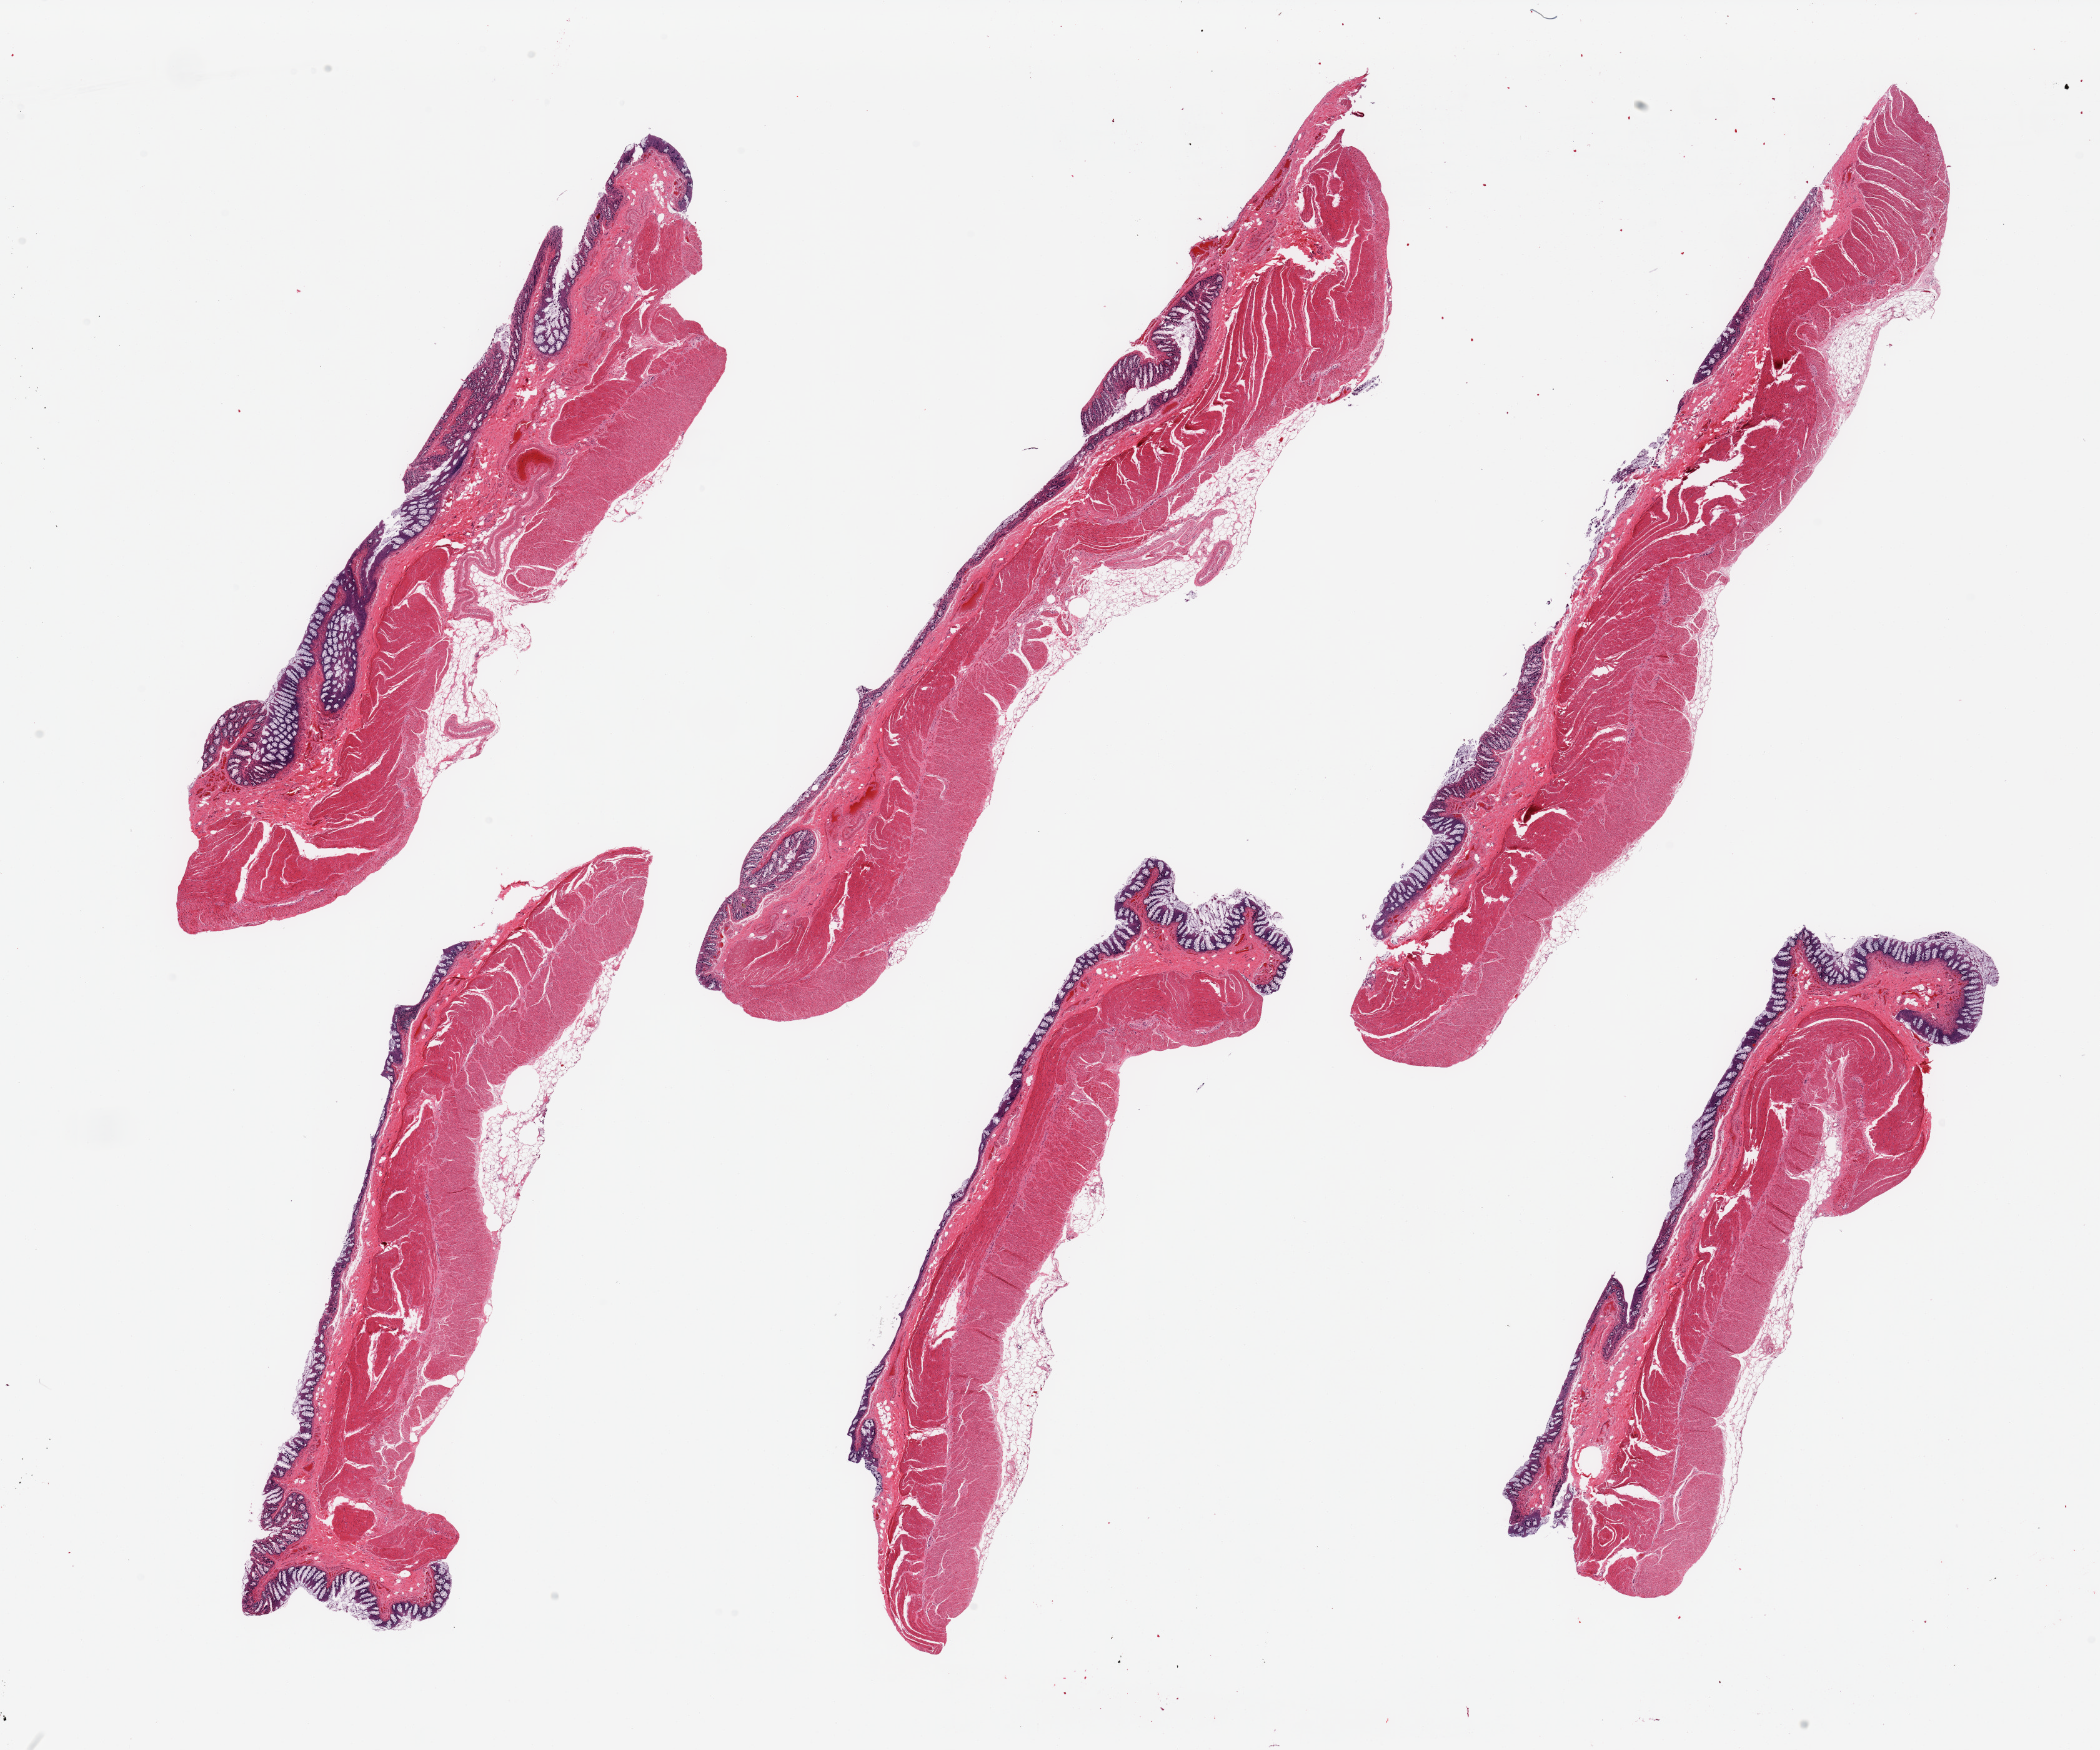
Digitized hematoxylin and eosin (H&E)-stained section, a low-resolution overview of the entire scanned area, about 26.6 x 22.2 mm (slide scanned at 20x); PAXgene-fixed paraffin-embedded (PFPE) section; target tissue: transverse colon; tissue donor sample. Donor: male.
Pathologist's review note for this sample: 6 pieces glandular mucosa with advanced autolysis, partially sloughing.